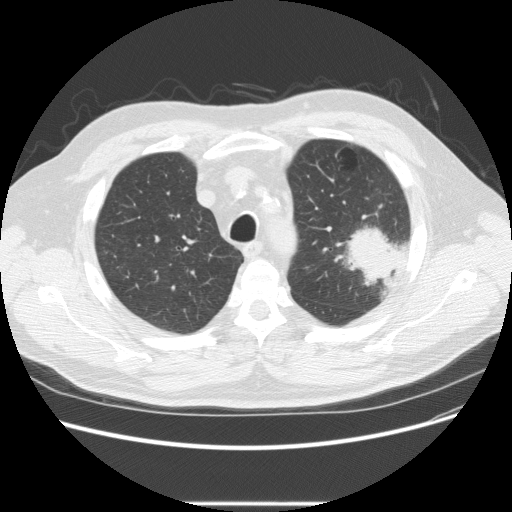
Axial slice from a low-dose chest CT screening exam. Baseline annual screen. Lung window (W 1500 / L -600 HU). 2.5 mm slice thickness. 120 kVp. 512 × 512 image matrix, field of view 380 × 380 mm. Male participant, aged 73 years at enrolment. Former smoker at enrolment.
Expert reader's lesion annotation, bounding box [x1, y1, x2, y2] px = [332, 215, 414, 285]. The screening reader recorded 2 non-calcified nodules or masses ≥4 mm on this exam (left upper lobe, right upper lobe); which of them this box marks is not recorded. Participant outcome: lung cancer diagnosed 11 days after this screen — bronchiolo-alveolar adenocarcinoma, NOS, other location, well differentiated (G1), stage IV (AJCC 6th edition).